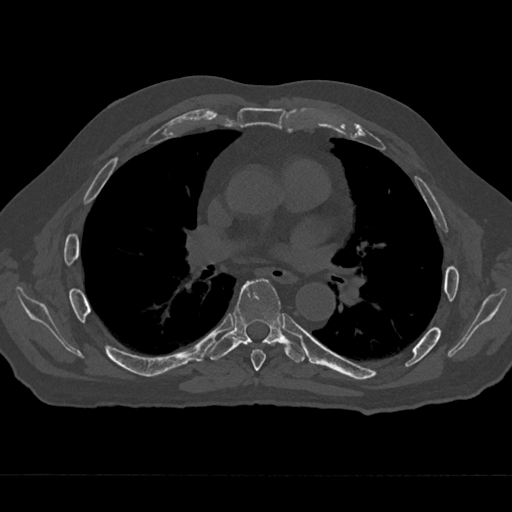
CT including the spine, one axial slice. Position 392 of 797 along the scan axis. Reconstruction kernel Br40s/3. 120 kVp. Bone window (W 1800 / L 400 HU). 0.5 mm slice thickness. 512 × 512 image matrix, field of view 377 × 377 mm. Male patient, age 75 years. Case-level facts recorded for this patient, not image findings: primary cancer: renal.
Structures marked on this image (semi-automatically segmented with operator editing):
- T6 vertebra: bounding box <251,349,266,371> (left, top, right, bottom; pixels)
- T7 vertebra: <208,278,305,362>